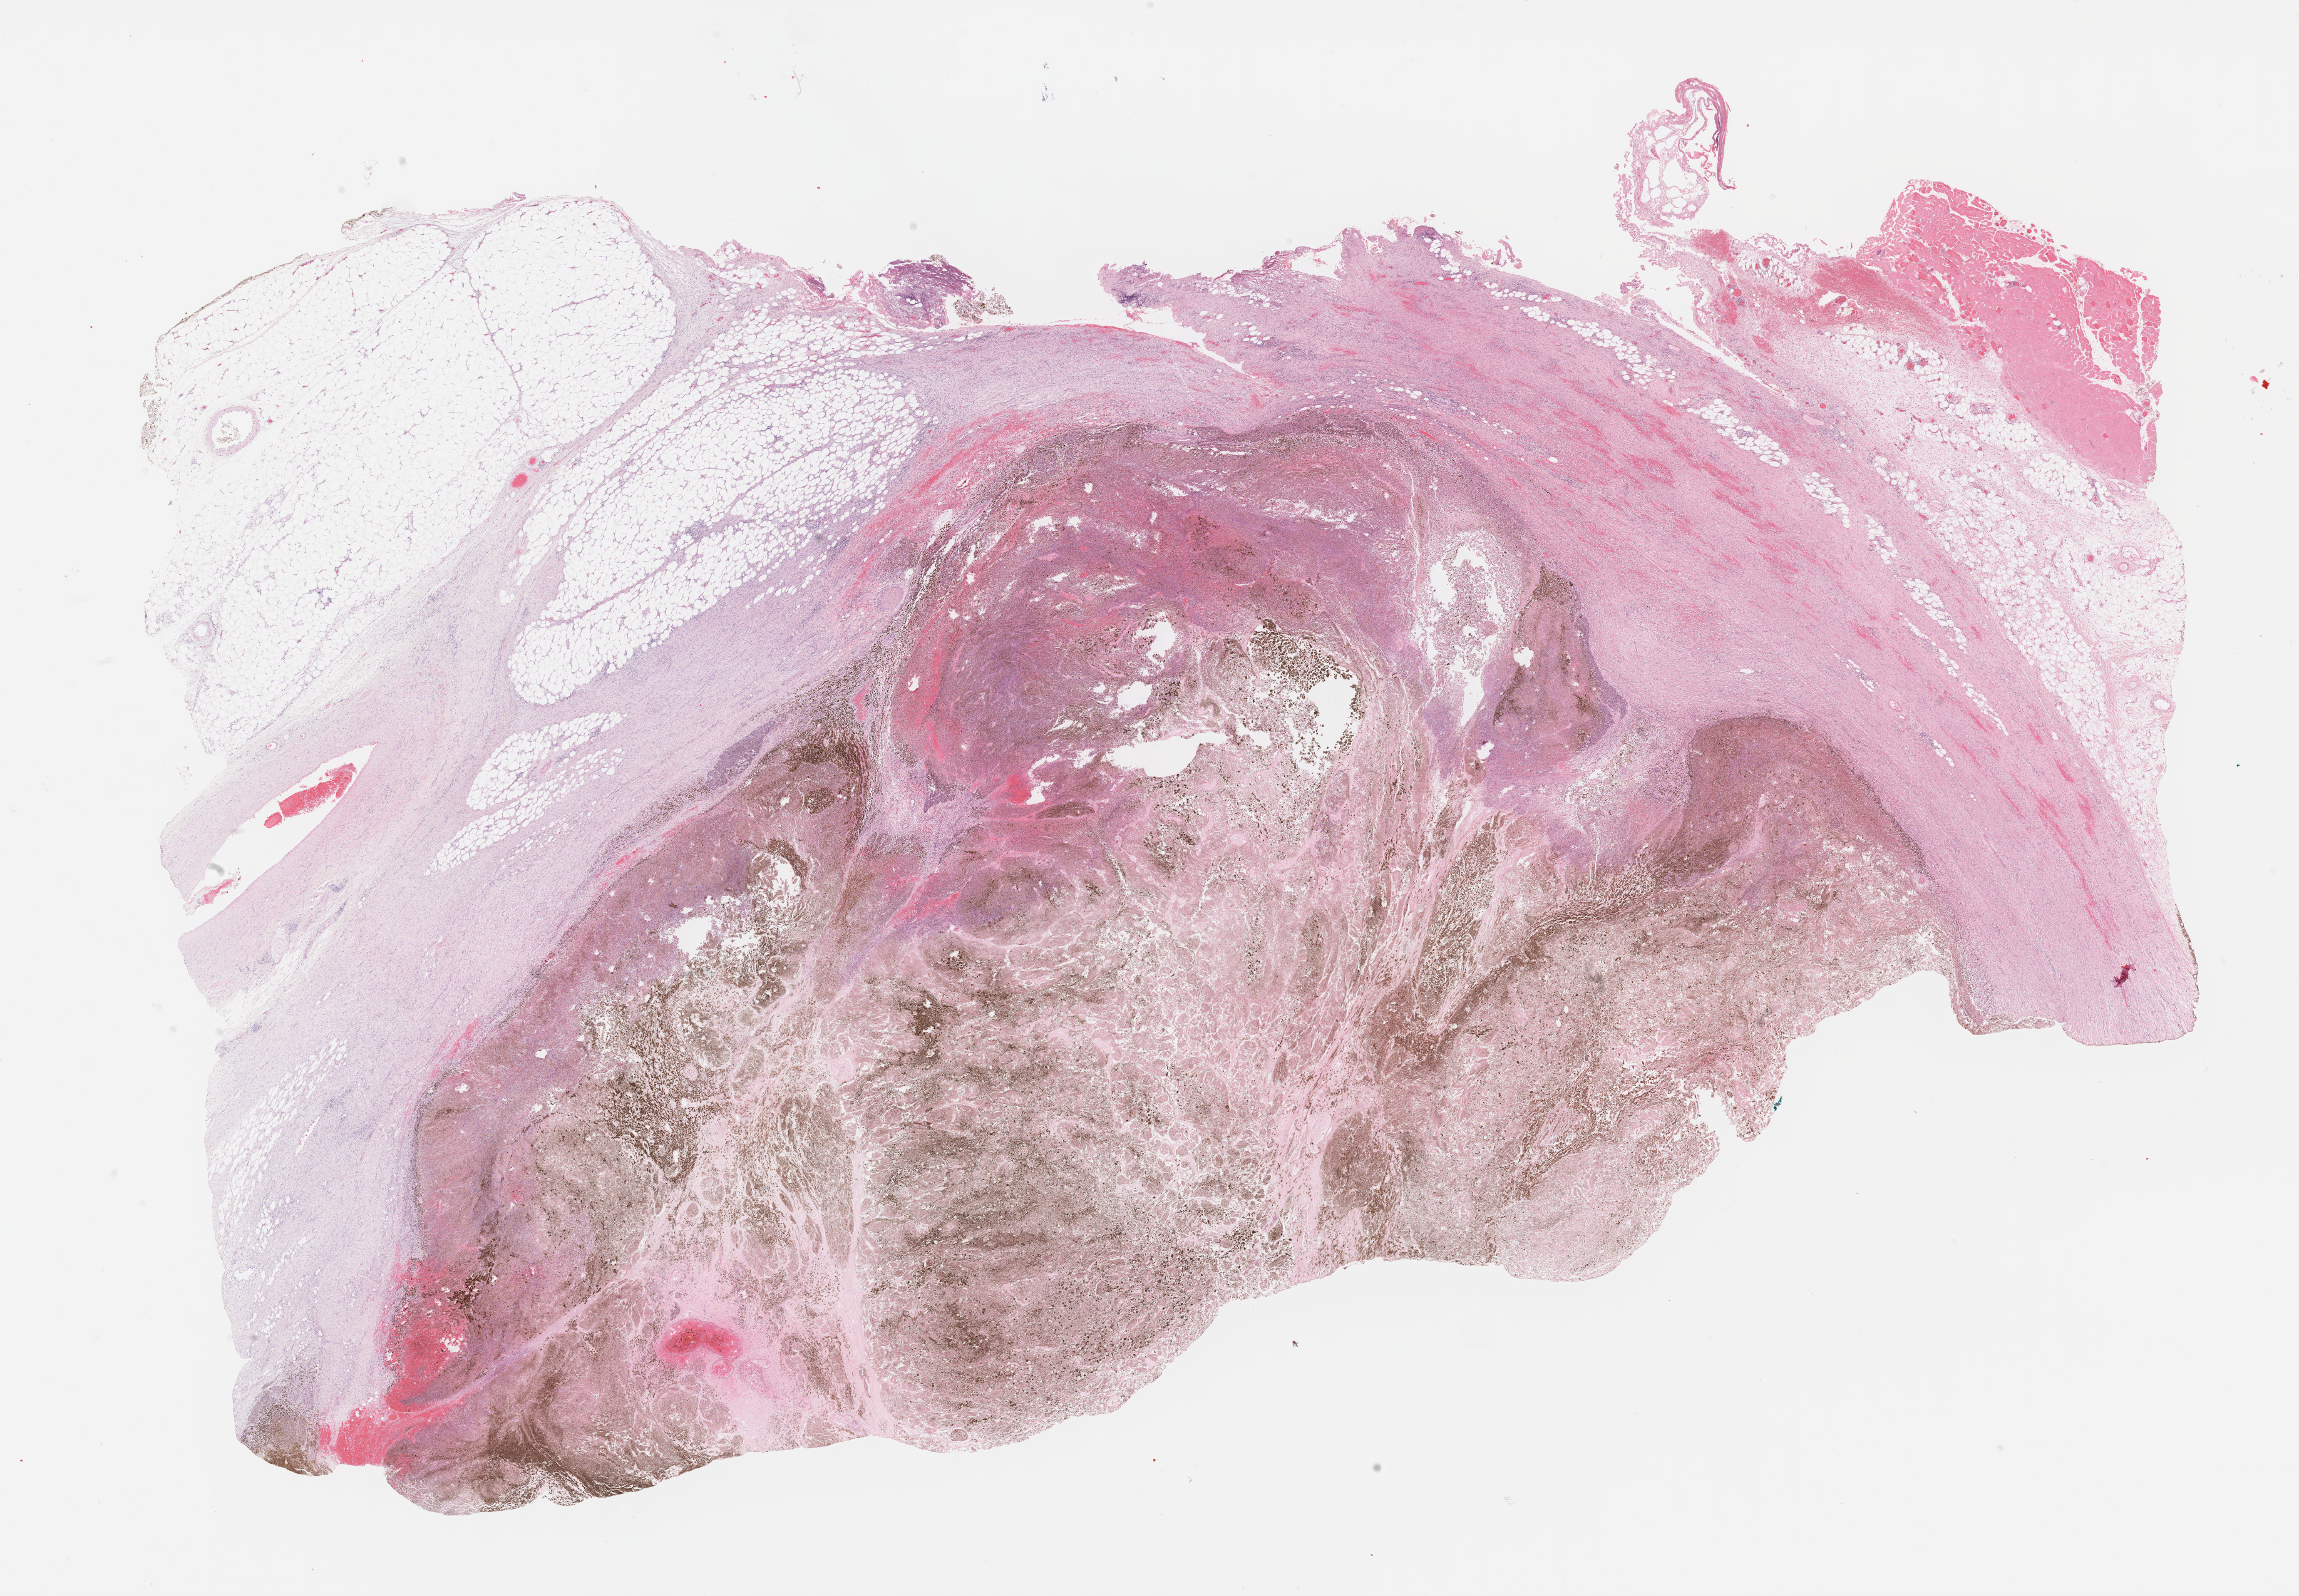
Whole-slide histology image, H&E-stained, whole scanned area (about 29.7 x 20.6 mm, slide scanned at 40x) shown as a low-resolution overview. FFPE section. Metastatic tumour sample, sampled site: lymph nodes of inguinal region or leg. Male, age 37 years at initial diagnosis.
This section: metastatic tumour tissue. Patient diagnosis: Superficial spreading melanoma.